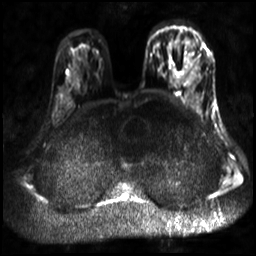
Breast MRI, one axial slice. Slice 21 of 30 in the series (ordered by position). Diffusion-weighted series; image 2 of 4 stored at this slice position (different b-values; order by instance number). 3 T. 4 mm slice thickness. 256 × 256 image matrix. Female patient.
Outlined on this slice (outlined manually by an expert reader):
- tumour on diffusion-weighted imaging: bounding box [x1, y1, x2, y2] px = [187, 43, 198, 74]